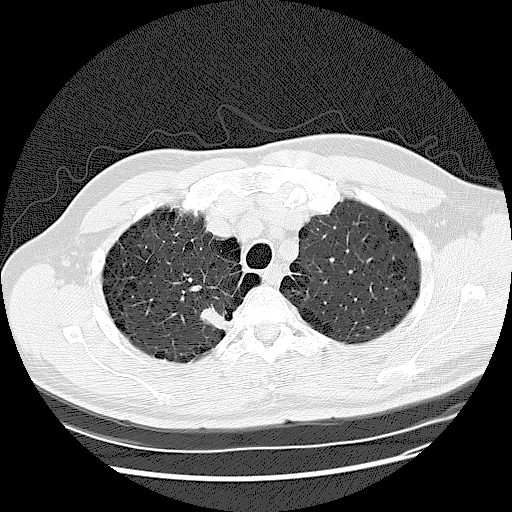
Low-dose screening chest CT, one axial slice. Position 107 of 132 along the scan axis. Lung window (W 1500 / L -600 HU). 2.5 mm slice thickness. 512 × 512 image matrix.
Structures marked on this image (manually delineated by an expert):
- lesion 1 (tumor, upper lobe of right lung): bounding box <200,304,231,330> (left, top, right, bottom; pixels)